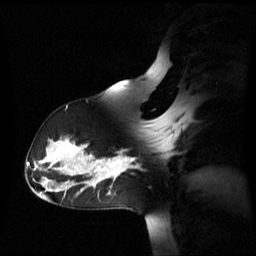
Breast MRI (dynamic contrast-enhanced), one sagittal slice; position 39 of 60 along the scan axis; dynamic contrast-enhanced series, image 2 of 3 at this slice position (ordered by acquisition); 1.5 T; TE 4.2 ms, TR 8.4 ms; 2.6 mm slice thickness; 256 × 256 image matrix. Female patient, age 39 years. From the clinical record (not read from this slice): setting: breast cancer imaged before/during neoadjuvant chemotherapy; receptor status: triple-negative.
Annotated regions visible in this slice (semi-automatic segmentation, software-assisted and operator-edited):
- analysis volume of interest (the breast-tissue region the enhancement analysis was run in; not a lesion): box from (x=105, y=157) to (x=134, y=179) px
- tumour enhancement mask (voxels above the 70 % enhancement threshold inside the analysis volume of interest): (x=105, y=157)–(x=134, y=178)